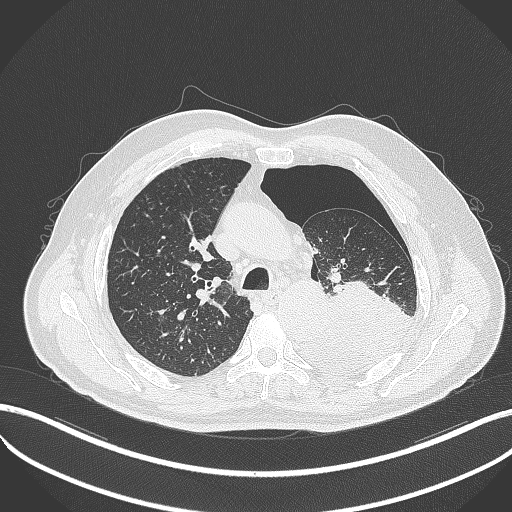
Chest CT, one axial slice. Slice 358 of 464 in the series (ordered by position). 120 kVp. Lung window (W 1500 / L -600 HU). 512 × 512 image matrix, field of view 400 × 400 mm. Patient: male, 76 years. From the clinical record (not read from this slice): clinical TNM (as recorded): T3 N0 M1b.
Outlined on this slice (rectangle marked by the reading radiologist):
- lung tumour (recorded histology: adenocarcinoma): bounding box (x1, y1, x2, y2) in pixels: (293, 277, 415, 370)